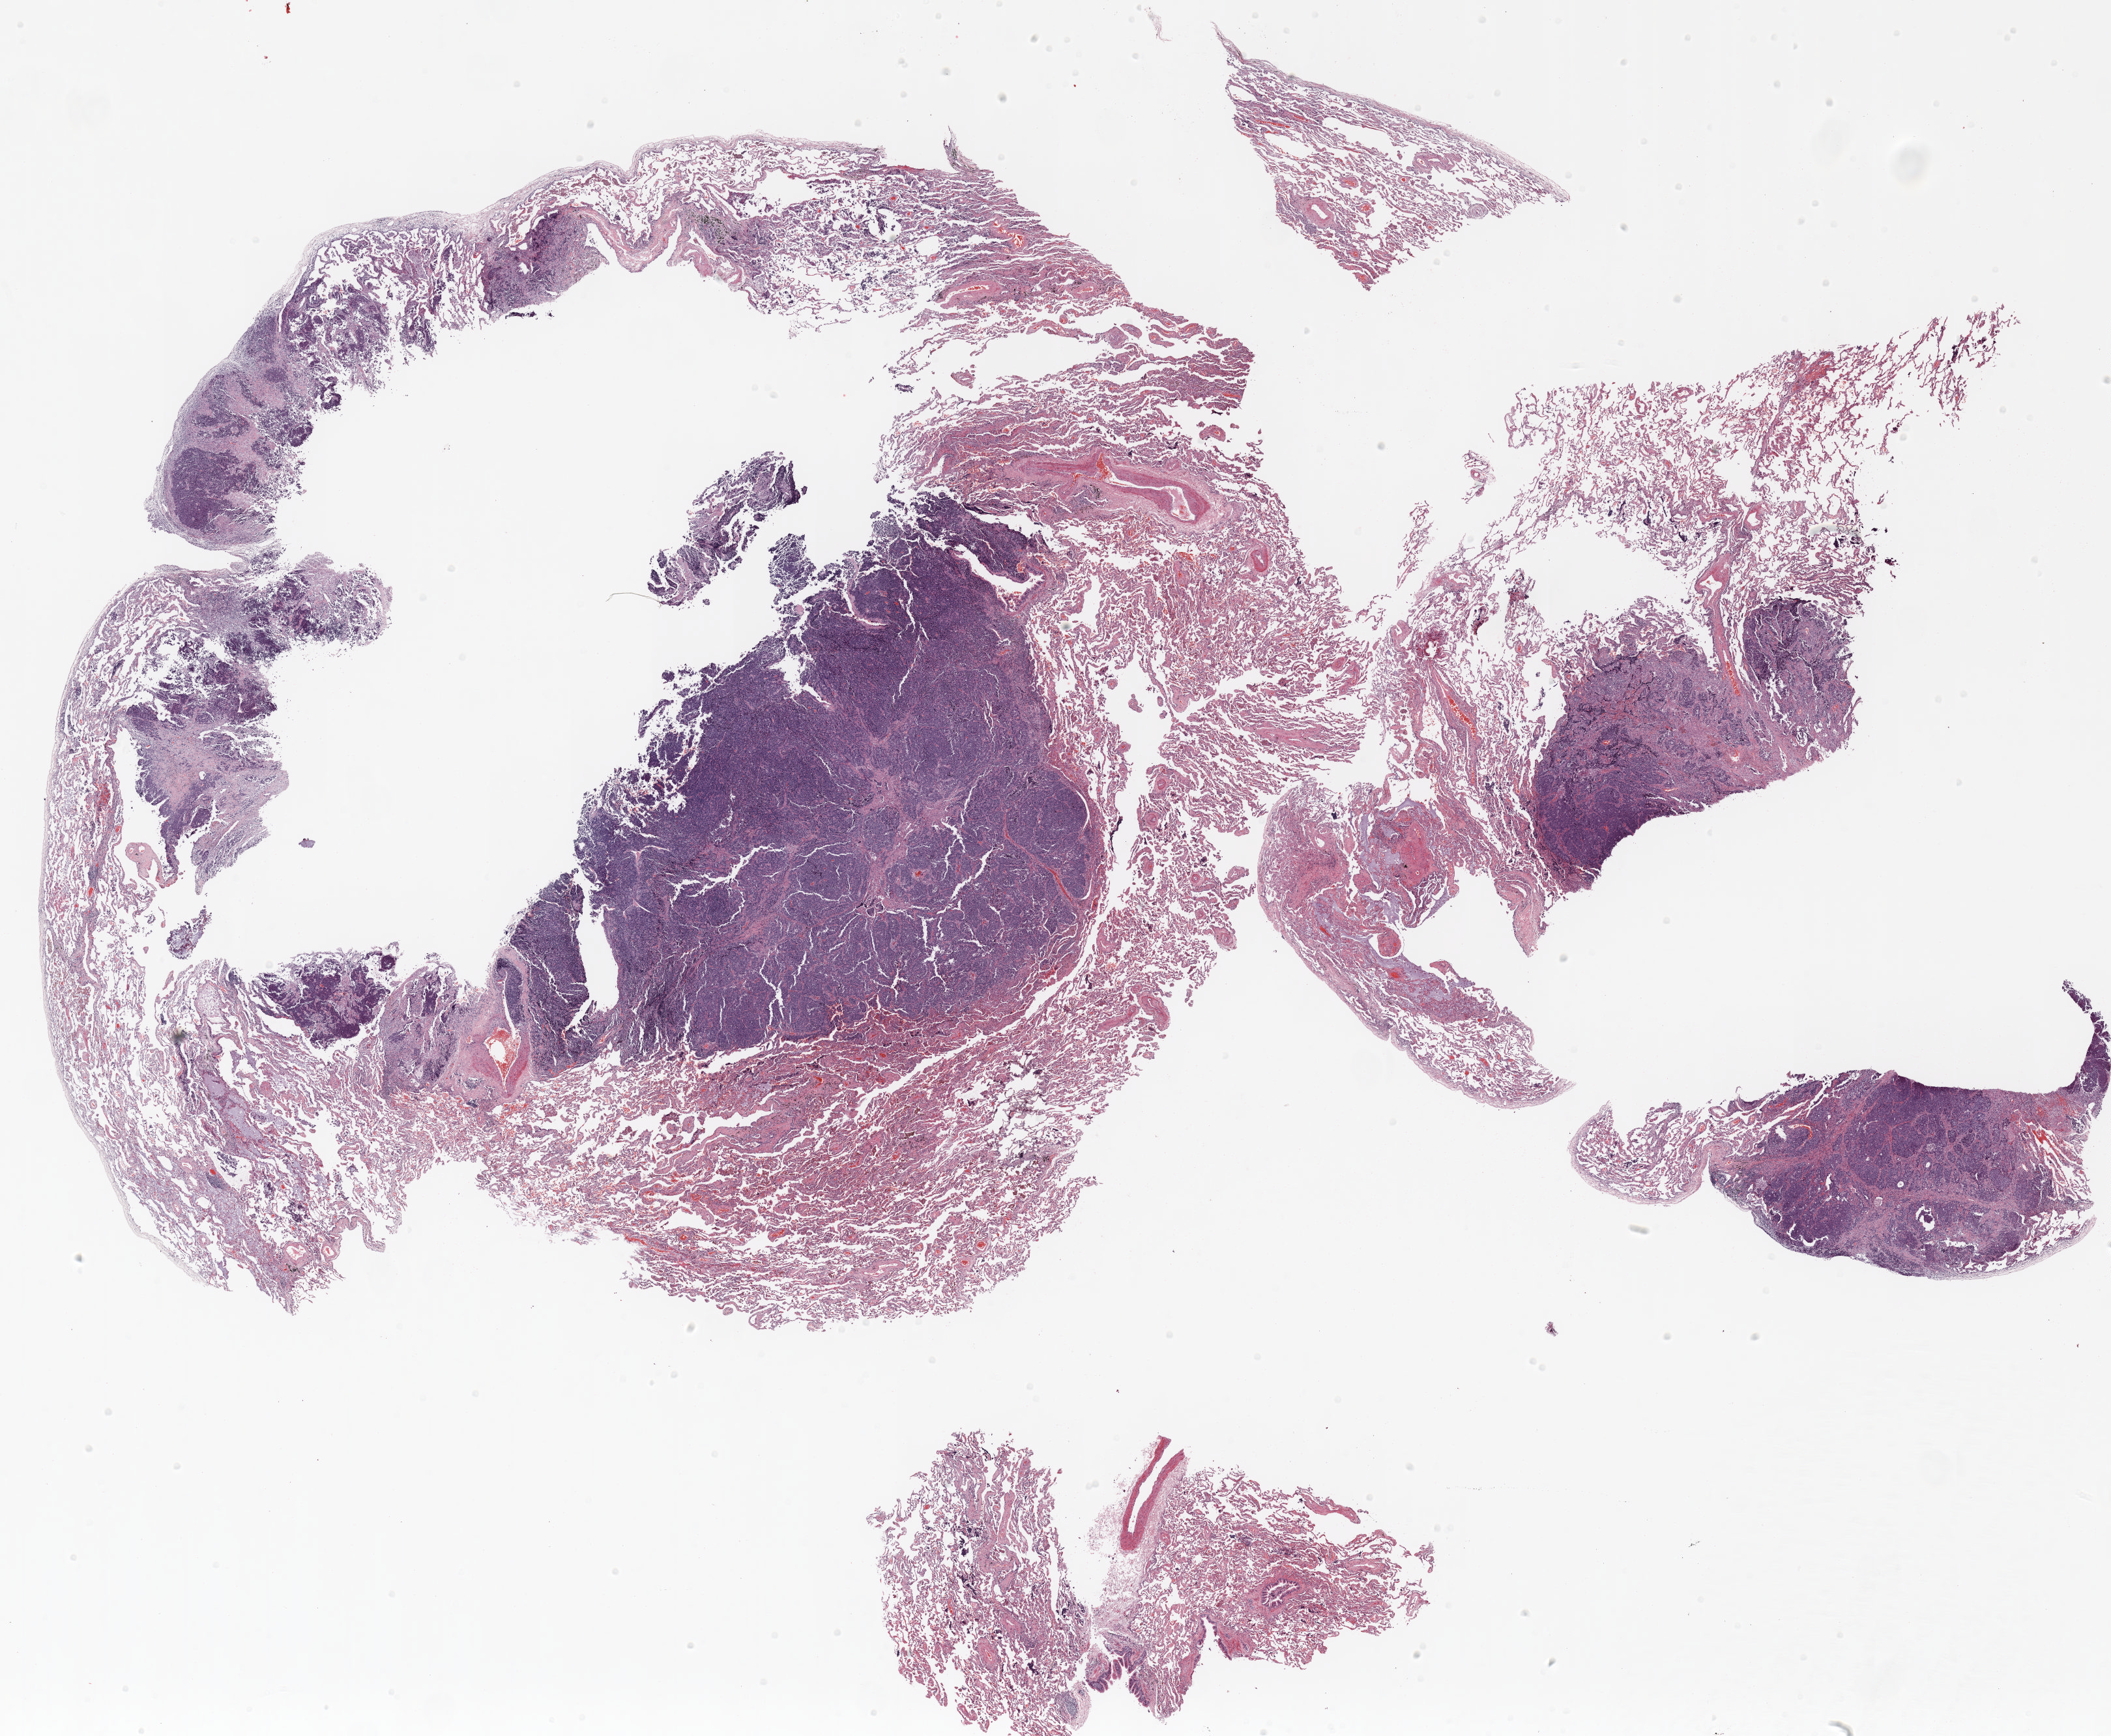
H&E-stained whole-slide image, shown as a low-resolution overview of the whole scanned area (about 26.0 x 21.4 mm); formalin-fixed paraffin-embedded (FFPE) section; lung tissue. Male, age 69 at enrolment. Grade: poorly differentiated (G3).
* participant's lung-cancer diagnosis: Large cell neuroendocrine carcinoma
* stage (AJCC 6th edition): IA
* ICD-O-3 topography: upper lobe of lung (C34.1)
* primary tumour location (clinical record): right upper lobe
* tumour size (pathology): 23 mm